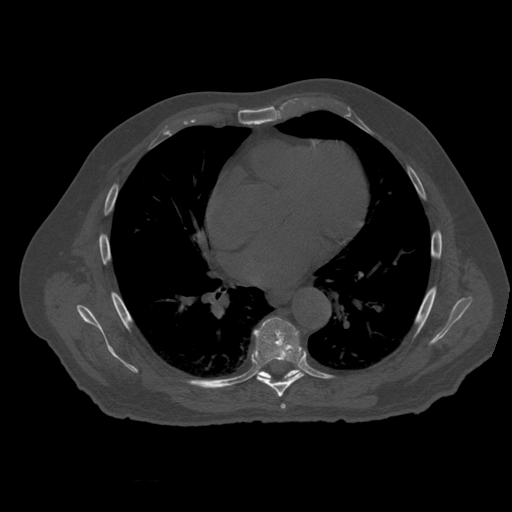
CT including the spine, one axial slice. Slice 355 of 399 in the series (ordered by position). 120 kVp. Bone window (W 1800 / L 400 HU). 512 × 512 image matrix, field of view 407 × 407 mm. Patient age 73 years. Case-level facts recorded for this patient, not image findings: primary cancer: prostate; vertebrae with lytic lesions (as recorded): L2.
Annotated regions visible in this slice (semi-automatically segmented with operator editing):
- T6 vertebra: bounding box [x1, y1, x2, y2] px = [281, 404, 286, 409]
- T7 vertebra: [253, 317, 304, 398]
- T8 vertebra: [259, 370, 300, 380]